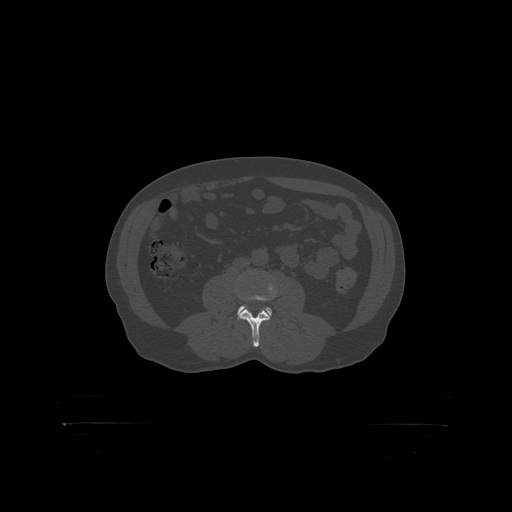
CT including the spine, one axial slice; slice 256 of 399 in the series (ordered by position); reconstruction kernel STANDARD; 120 kVp; bone window (W 1800 / L 400 HU); 1.25 mm slice thickness; 512 × 512 image matrix, field of view 650 × 650 mm. Male patient, age 46 years. From the clinical record (not read from this slice): primary cancer: skin.
Annotated regions visible in this slice (semi-automatic segmentation, software-assisted and operator-edited):
- L3 vertebra: box from (x=240, y=283) to (x=277, y=319) px
- L4 vertebra: (x=238, y=306)–(x=273, y=316)